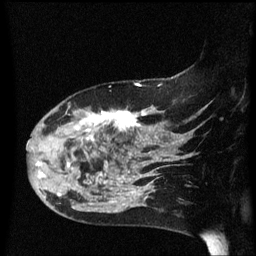
Breast MRI (dynamic contrast-enhanced), one sagittal slice; position 43 of 60 along the scan axis; dynamic contrast-enhanced series, image 2 of 3 at this slice position (ordered by acquisition); 1.5 T; TE 4.2 ms, TR 8.4 ms; 2.2 mm slice thickness; 256 × 256 image matrix. Female patient, age 47 years.
Structures marked on this image (semi-automatically segmented with operator editing):
- analysis volume of interest (the breast-tissue region the enhancement analysis was run in; not a lesion): bounding box [x1, y1, x2, y2] px = [28, 97, 149, 206]
- tumour enhancement mask (voxels above the 70 % enhancement threshold inside the analysis volume of interest): [36, 111, 149, 197]